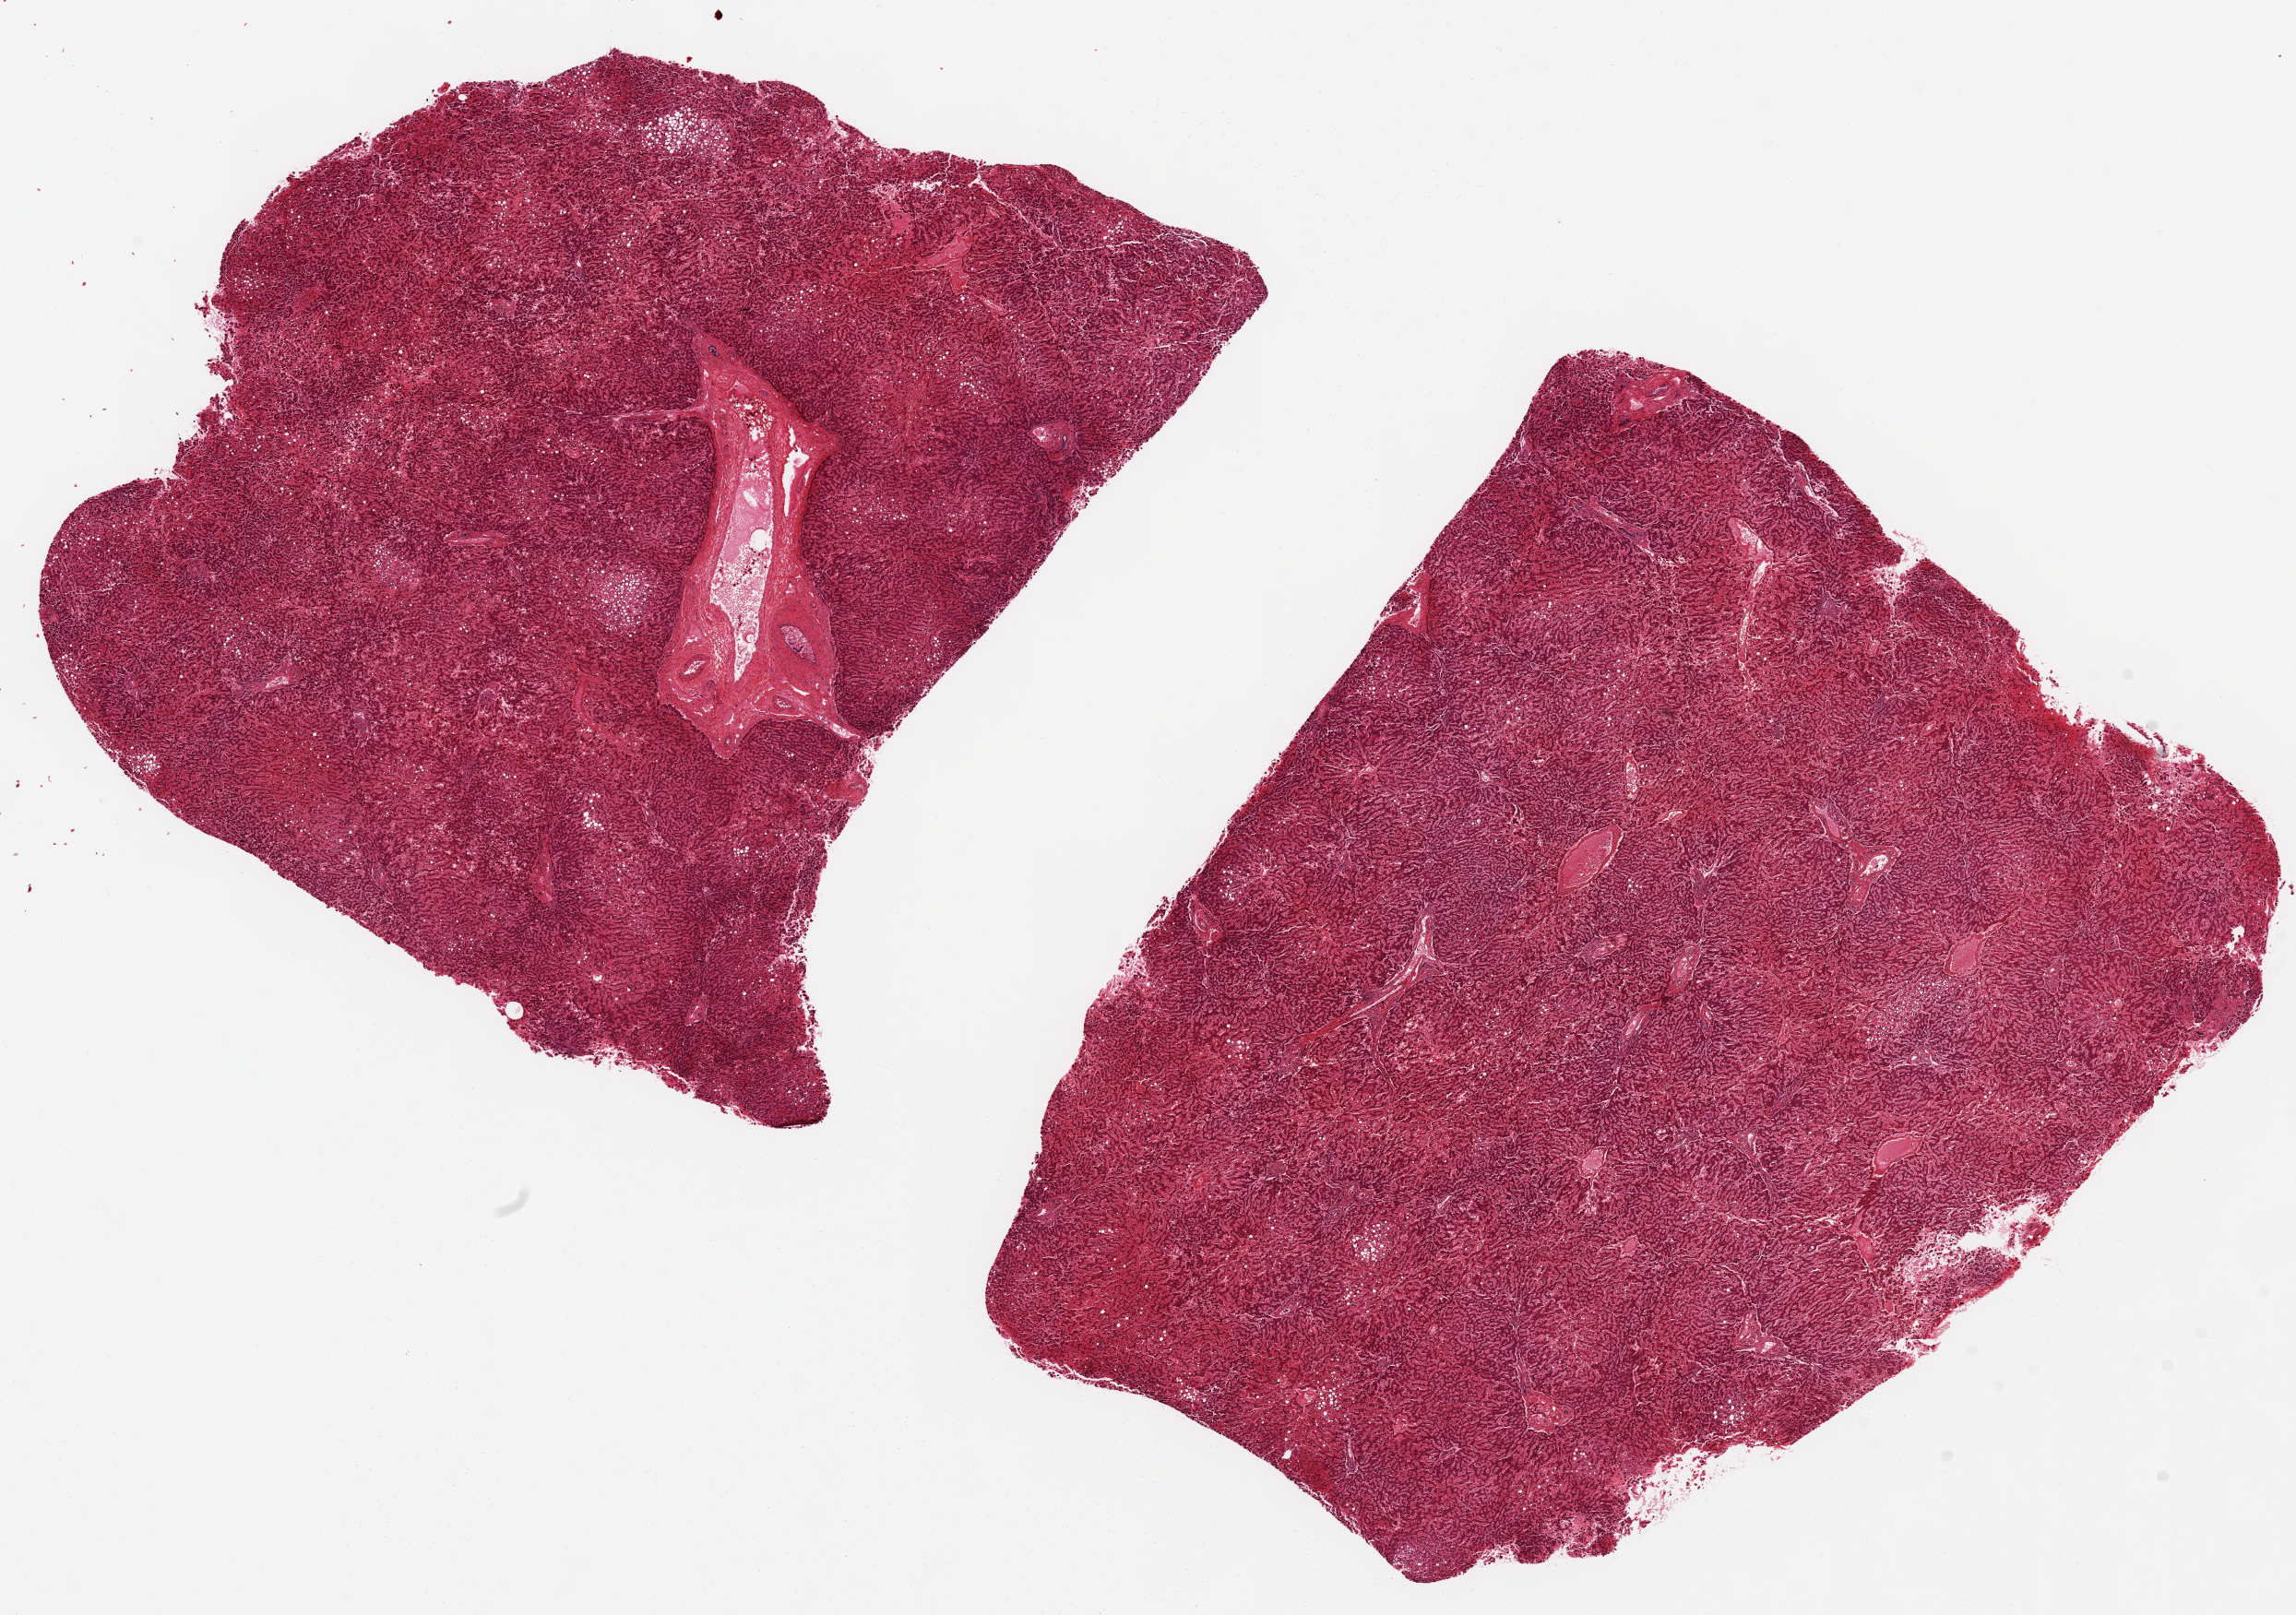
Haematoxylin and eosin whole-slide image, brightfield, low-resolution overview of the scanned area, about 19.7 x 13.9 mm (slide scanned at 20x). PAXgene-fixed paraffin-embedded (PFPE) section. Target tissue: liver. Donor tissue sample.
Review note (as recorded): 2 ~9x7.5mm aliquots, patchy mixed micro-and macro-vesicular steatosis, ~25%.